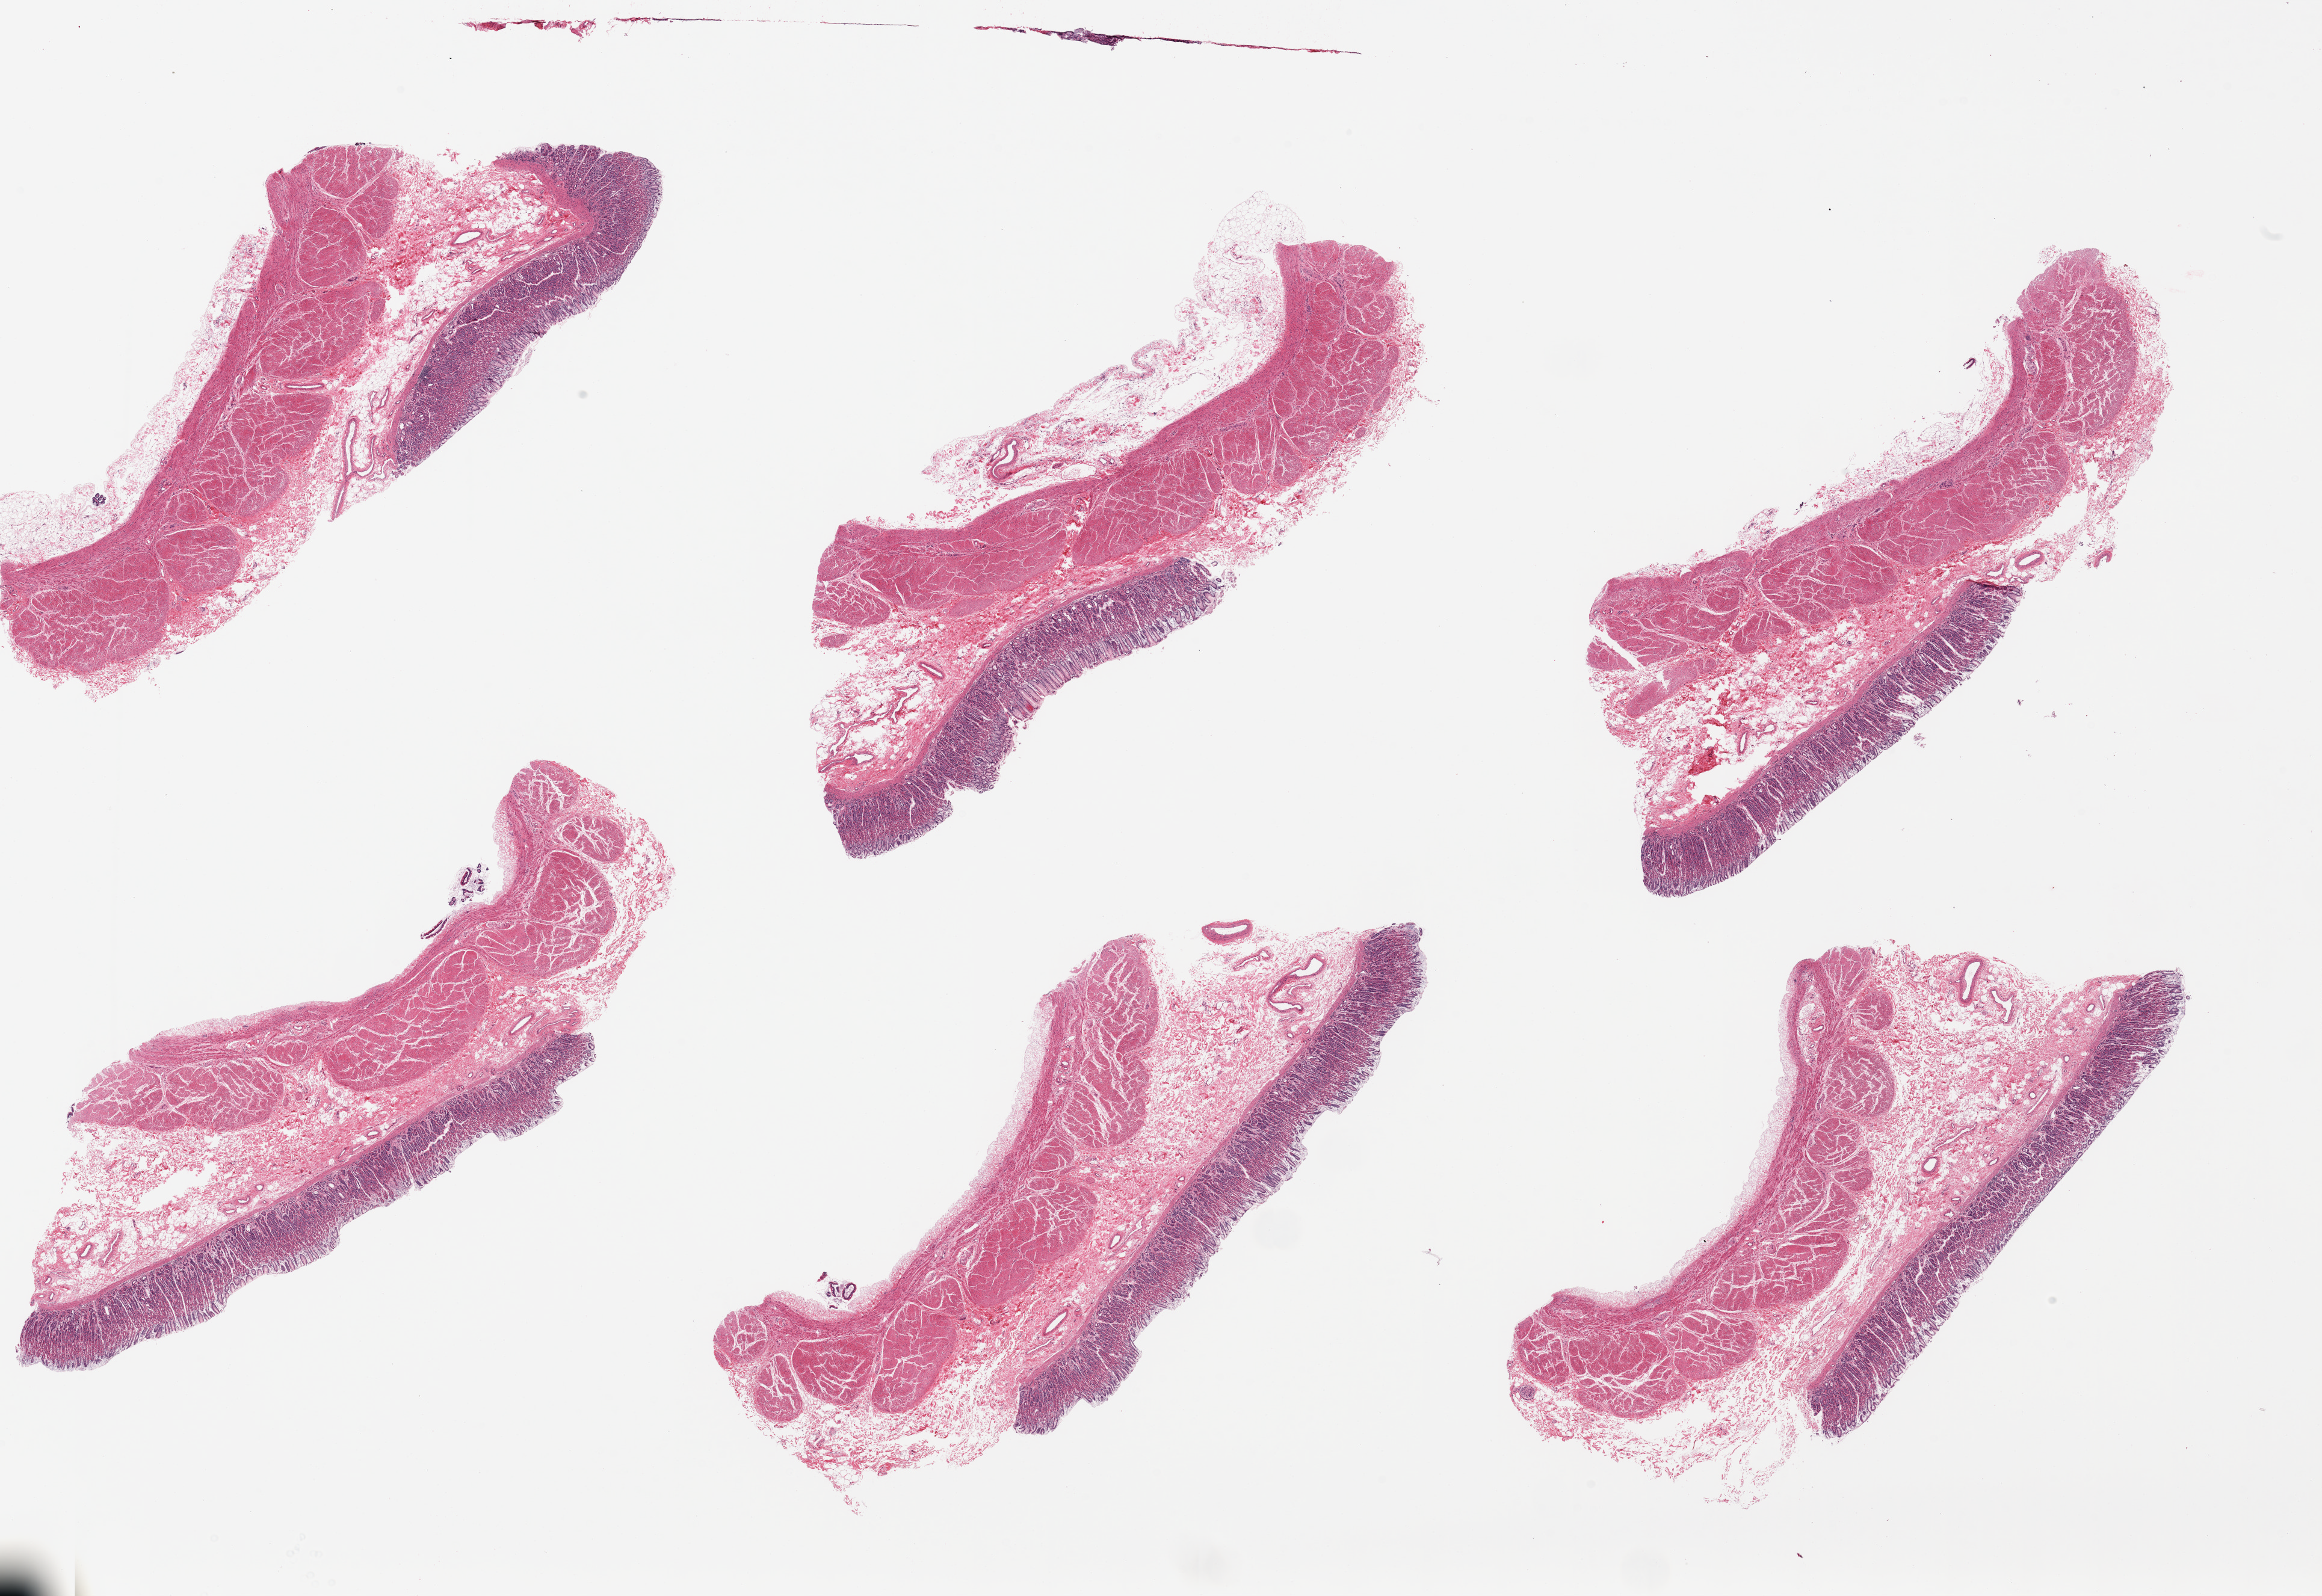
Digitized H&E-stained section, low-resolution overview of the scanned area, about 30.5 x 21.0 mm, PAXgene-fixed paraffin-embedded (PFPE) section, section of stomach (target tissue), donor tissue sample. Donor sex: male.
Reviewer comment on this tissue sample: 6 pieces. Mucosa is discontinuous but where present is well-preserved, ~20-30% thickness.